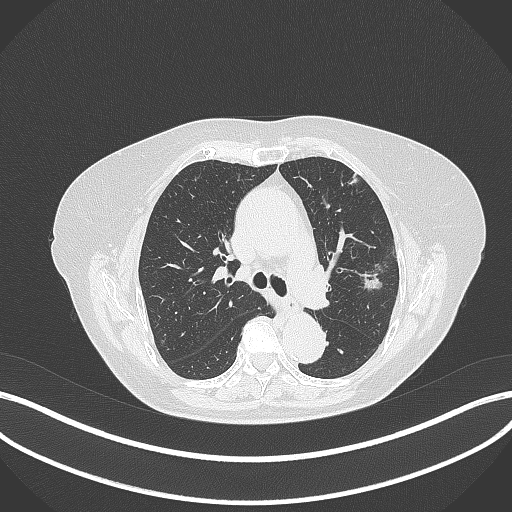
Chest CT, one axial slice. Slice 214 of 316 in the series (ordered by position). 120 kVp. Lung window (W 1500 / L -600 HU). 1 mm slice thickness. 512 × 512 image matrix, field of view 400 × 400 mm. Female patient, age 75 years. From the clinical record (not read from this slice): clinical TNM (as recorded): T1c N0 M0.
Structures marked on this image (bounding box drawn by a radiologist):
- lung tumour (recorded histology: adenocarcinoma): bounding box (x1, y1, x2, y2) in pixels: (356, 263, 383, 294)